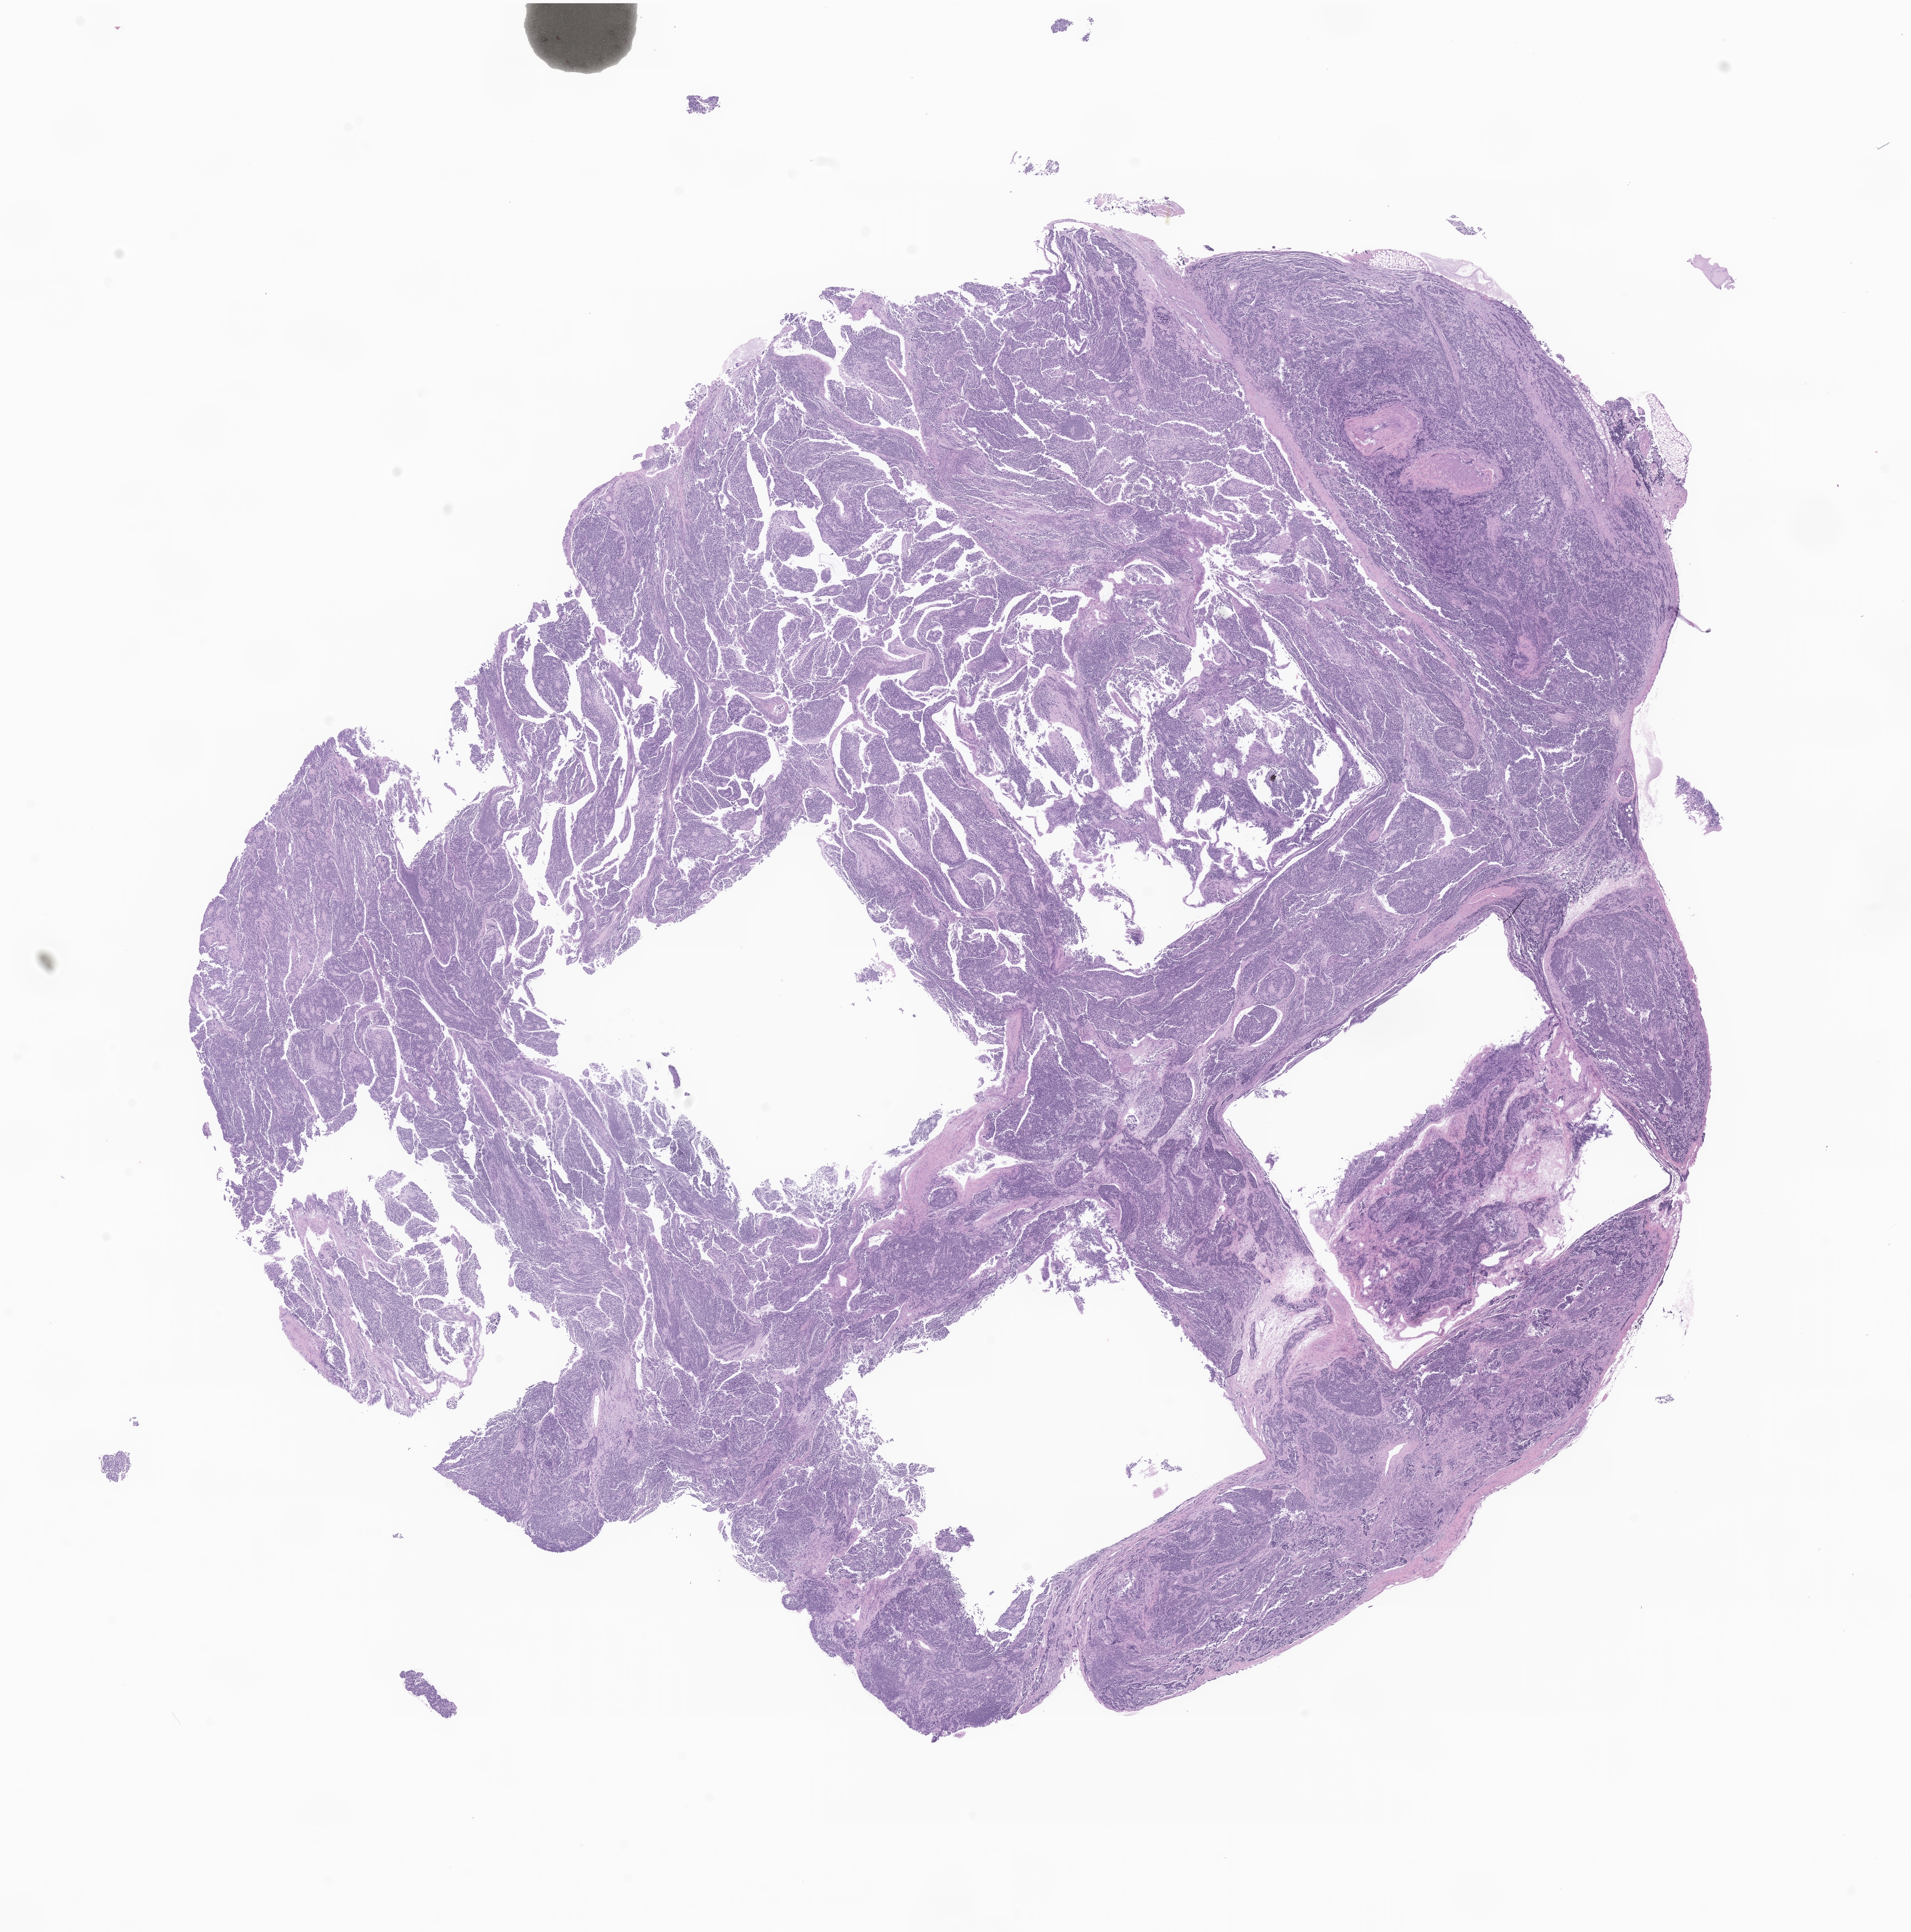
Whole-slide image, H&E stain of tumor tissue from the thorax, a low-resolution overview of the entire scanned area, about 18.6 x 18.8 mm, formalin-fixed paraffin-embedded section. Patient female; age 253 days.
- diagnosis: Neuroblastoma, NOS